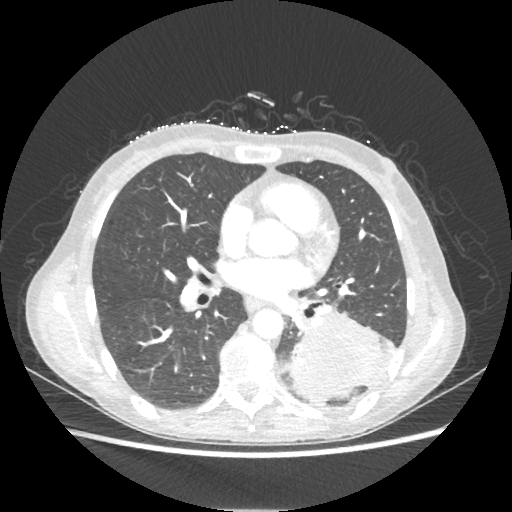
Chest CT, one axial slice. Position 108 of 221 along the scan axis. Reconstruction kernel STANDARD. 80 kVp. Lung window (W 1500 / L -600 HU). 1.25 mm slice thickness. 512 × 512 image matrix, field of view 360 × 360 mm. Female patient, age 53 years. From the clinical record (not read from this slice): clinical TNM (as recorded): T3 N0 M0.
Annotated regions visible in this slice (rectangle marked by the reading radiologist):
- lung tumour (recorded histology: adenocarcinoma): bounding box <290,311,385,407> (left, top, right, bottom; pixels)